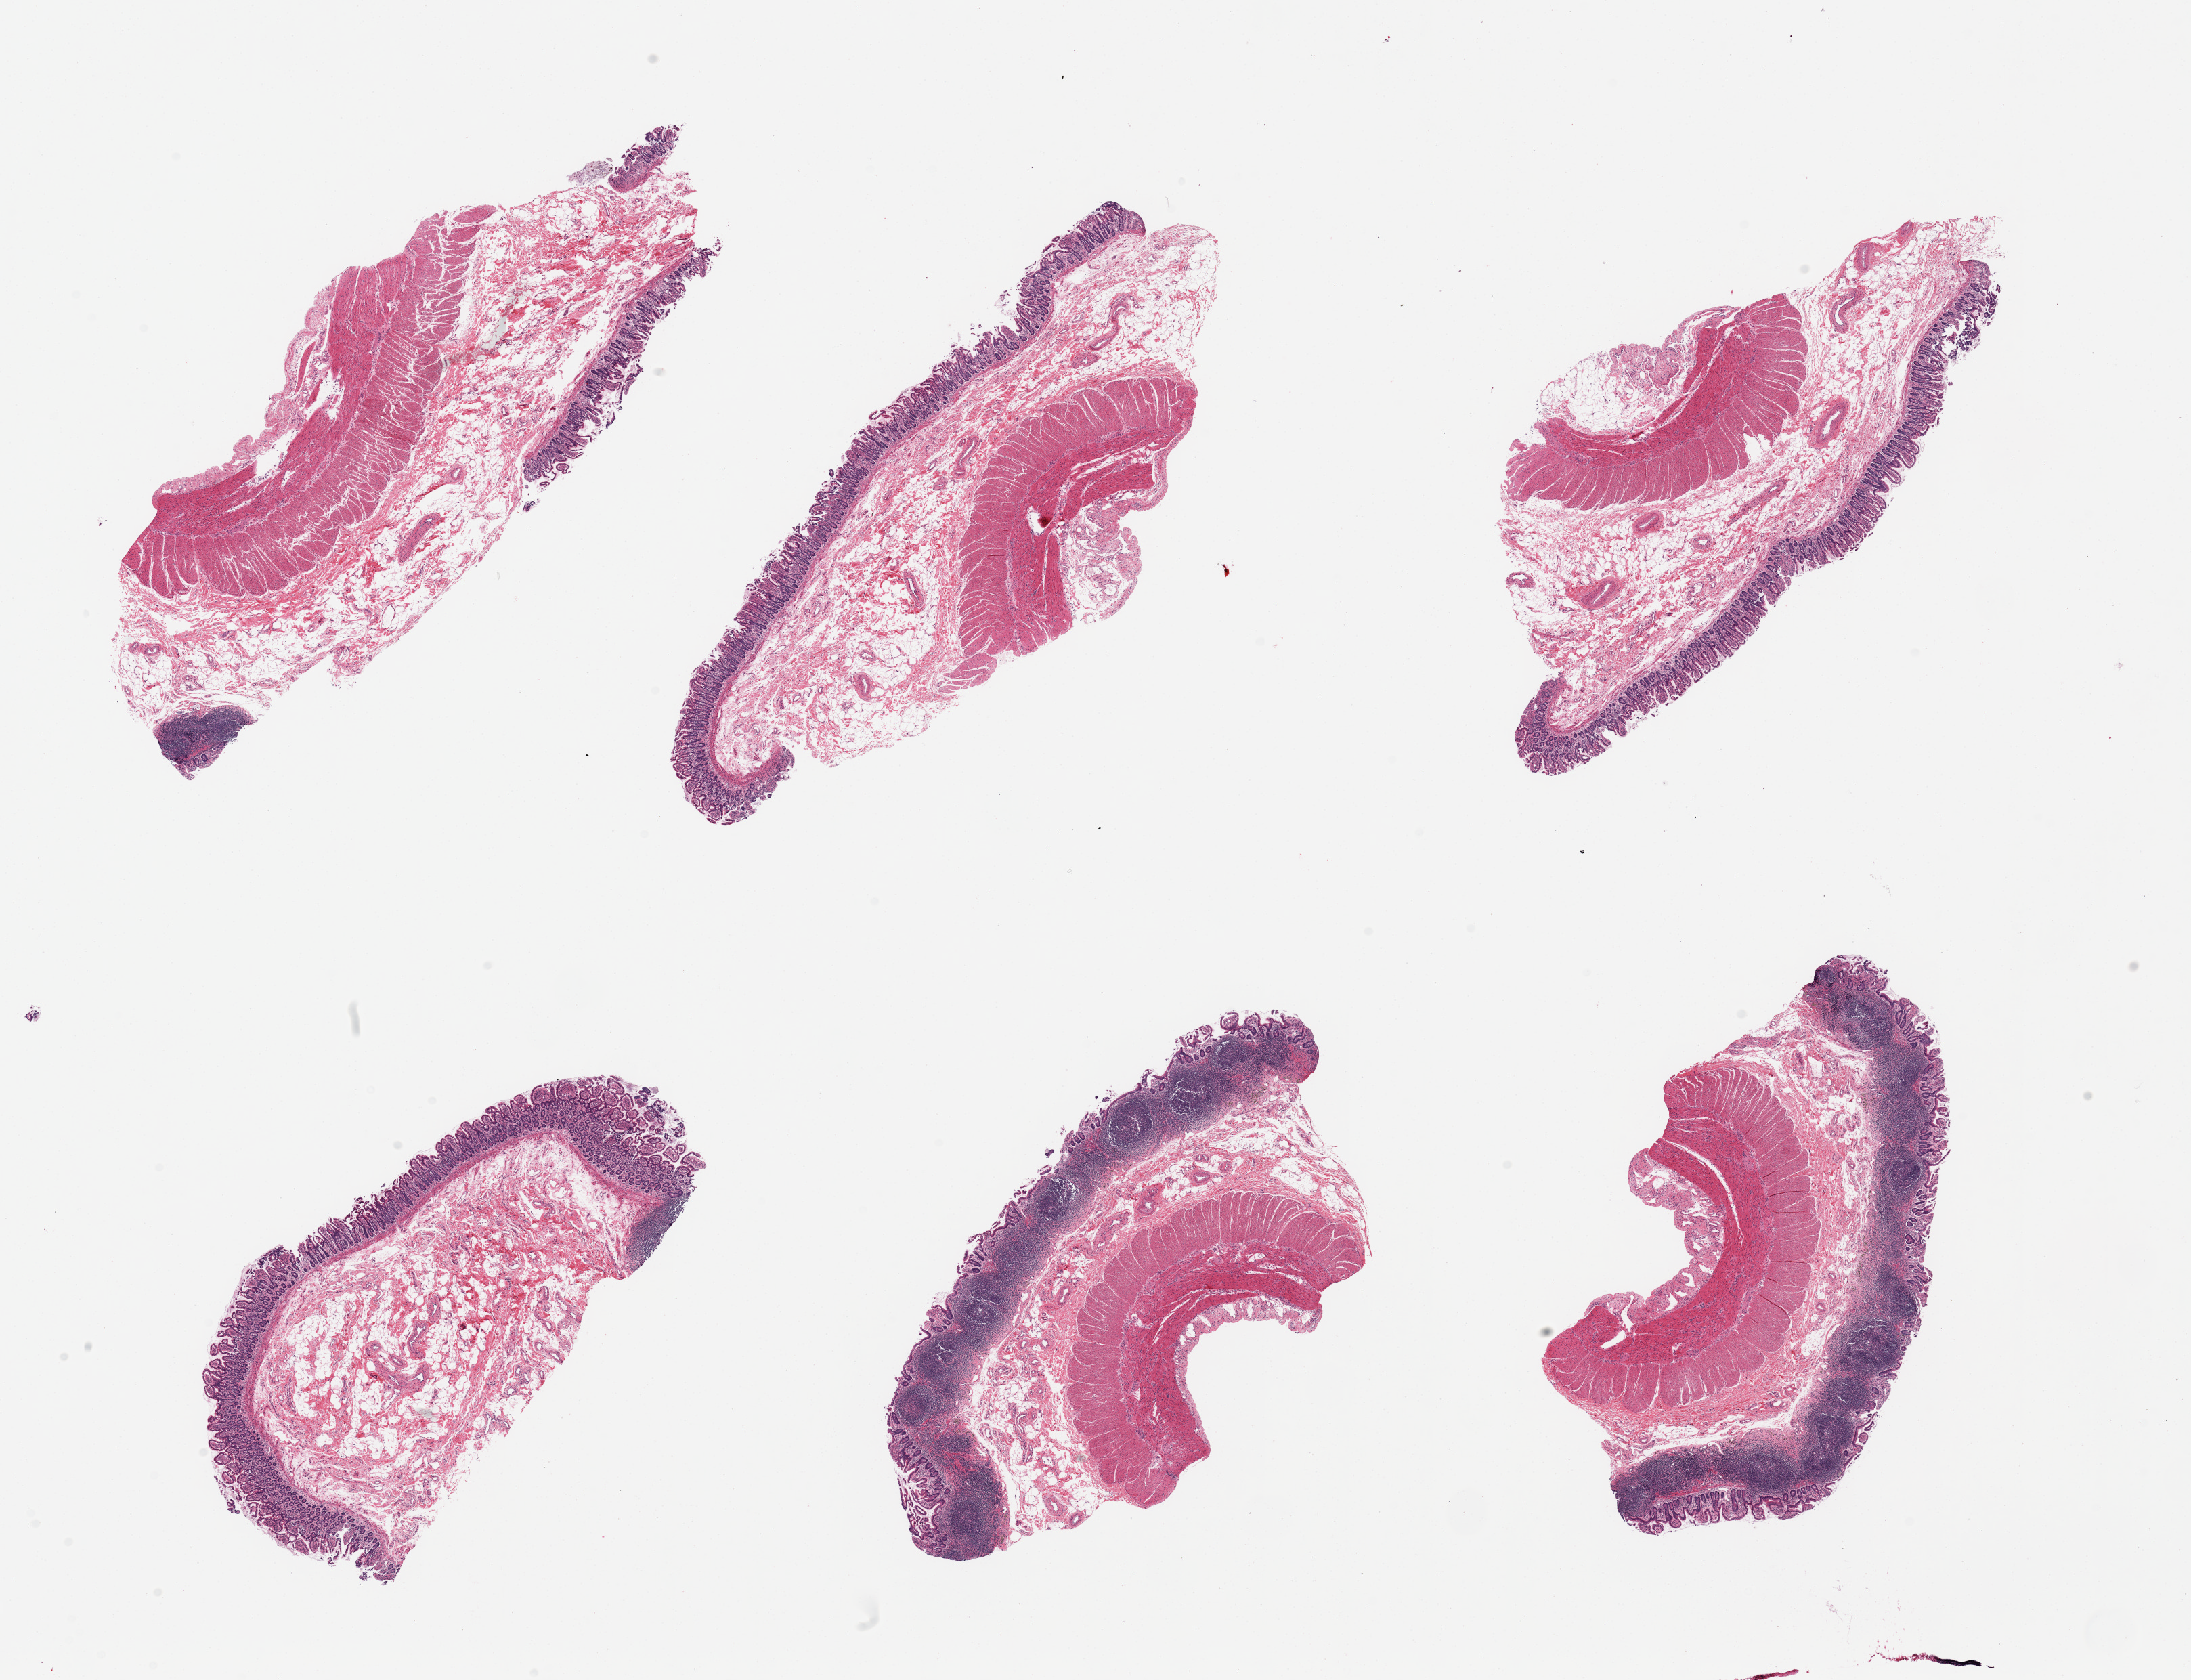
Digitized haematoxylin and eosin-stained section, low-resolution overview of the scanned area, about 25.6 x 19.6 mm (slide scanned at 20x), PAXgene-fixed paraffin-embedded (PFPE) section, section of ileum (target tissue), tissue donor sample. Donor sex: female.
• pathologist's review note for this sample: 6 pieces; lymphoid tissue in several pieces; muscularis propria included in 5